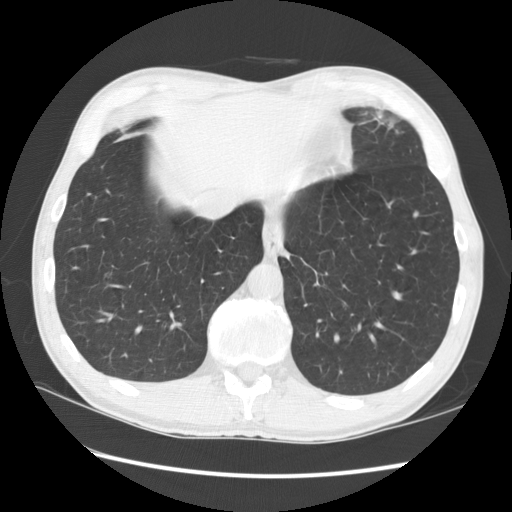
Low-dose screening chest CT, one axial slice; reconstruction kernel STANDARD; lung window (W 1500 / L -600 HU); 2.5 mm slice thickness; 512 × 512 image matrix, field of view 360 × 360 mm.
Outlined on this slice (expert manual segmentation):
- lesion 1 (tumor, lower lobe of left lung): bounding box [x1, y1, x2, y2] px = [373, 111, 378, 121]